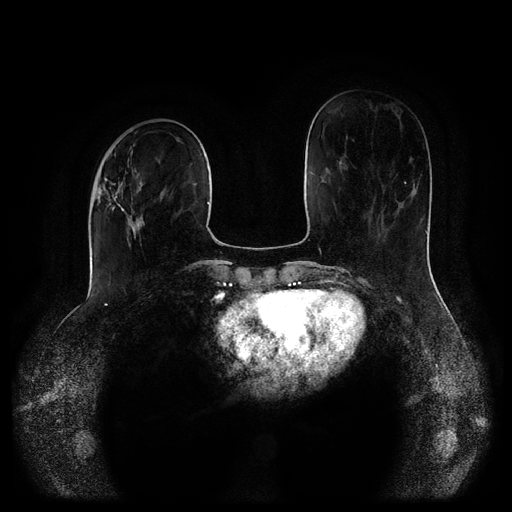
Breast MRI (dynamic contrast-enhanced, multi-phase), one axial slice. Position 34 of 116 along the scan axis. Dynamic contrast-enhanced series, time point 2 of 5 at this slice position (early post-contrast). 1.5 T. TE 2.6 ms, TR 5.2 ms. 2 mm slice thickness. 512 × 512 image matrix, field of view 380 × 380 mm. Patient: female, 52 years.
Structures marked on this image (semi-automatic segmentation, software-assisted and operator-edited):
- breast lesion (labelled 'tumour' in the annotation; benign lesions carry a separate 'benign' label): box from (x=97, y=171) to (x=144, y=247) px